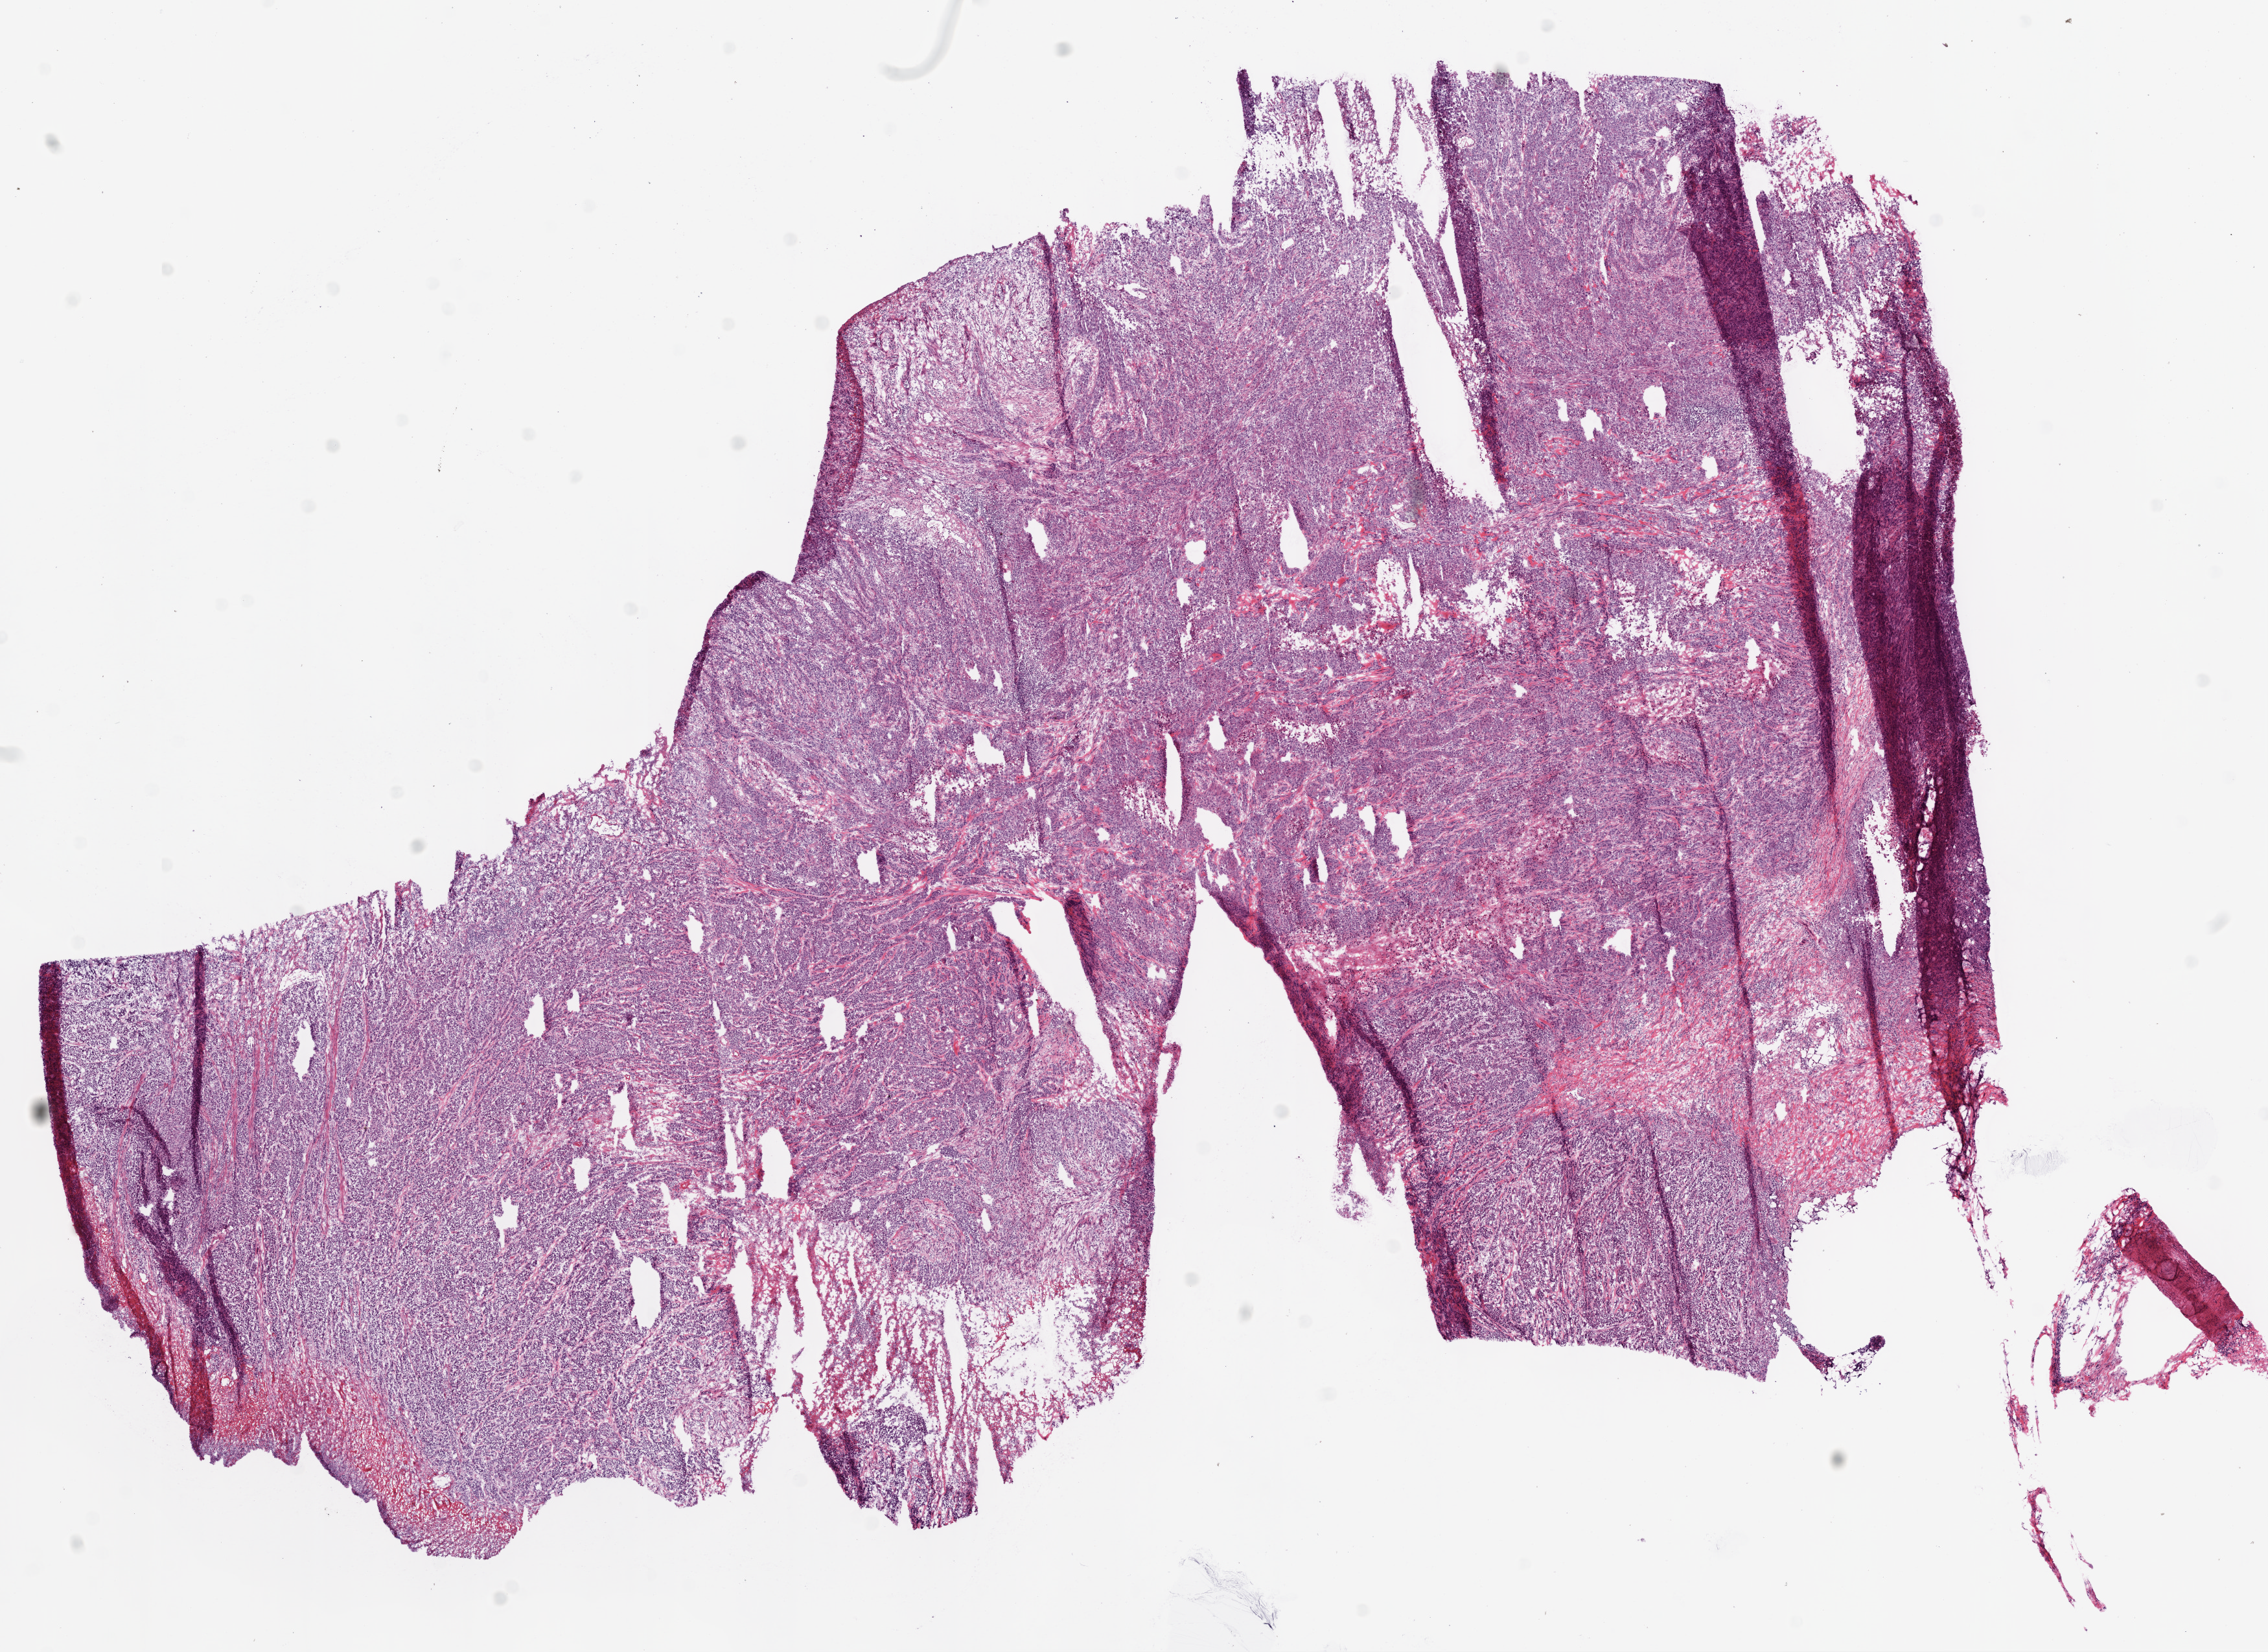
Digitized H&E tissue section (whole slide), whole scanned area (about 14.0 x 10.2 mm) shown as a low-resolution overview; frozen section from the bottom of the tissue portion; sample: primary tumour, colon. Patient: male, age at initial diagnosis 77 years. Pathologist review of this section (percent, as recorded): tumour cells 94%, tumour nuclei 90%, stromal cells 5%, necrosis 1%. Infiltration values recorded for this section: lymphocyte infiltration 1%.
- AJCC pathologic stage: II
- lymph nodes positive (case pathology): 0 of 12 examined
- diagnosis: Adenosquamous carcinoma
- TNM: T3 N0 M0